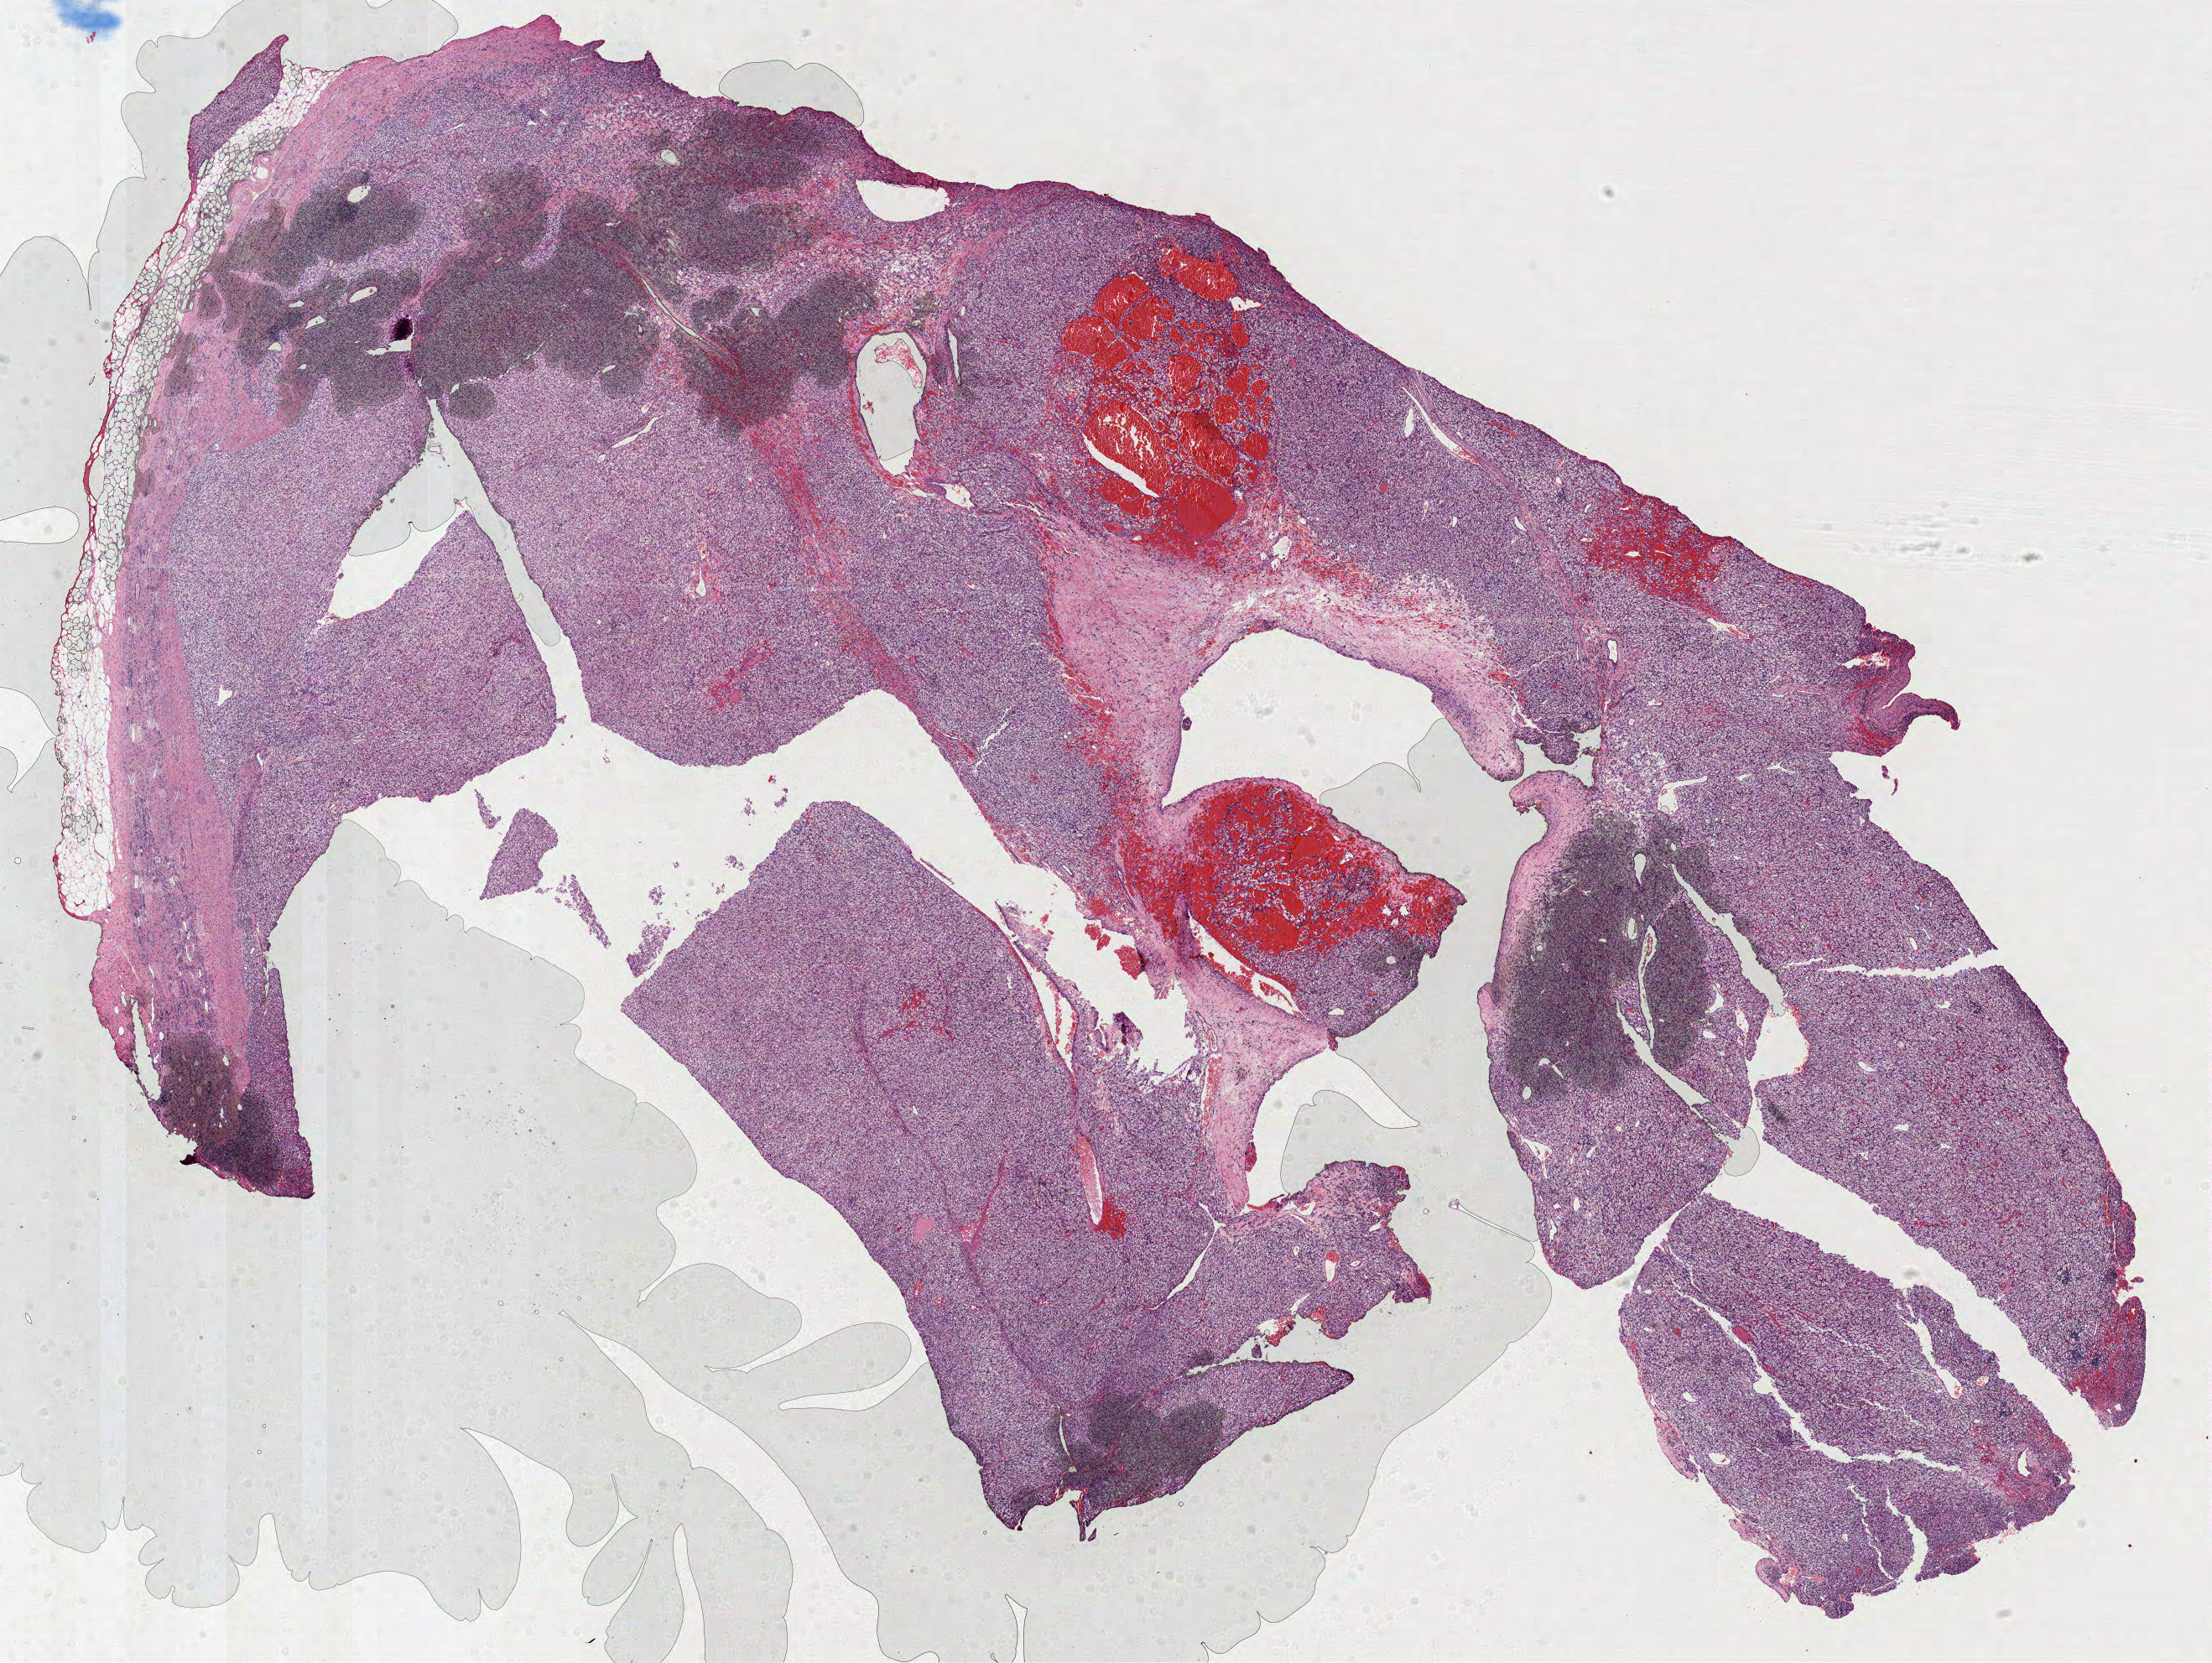
H&E-stained whole-slide image, shown as a low-resolution overview of the whole scanned area (about 21.3 x 16.0 mm, from a 40x scan); formalin-fixed paraffin-embedded (FFPE) diagnostic section; sample: primary tumour, kidney. Male patient; age at initial diagnosis 56 years. Histologic grade: G2 (moderately differentiated).
• histologic diagnosis: Clear cell adenocarcinoma, NOS
• TNM: T1b N0 M0
• AJCC pathologic stage: I (7th edition)